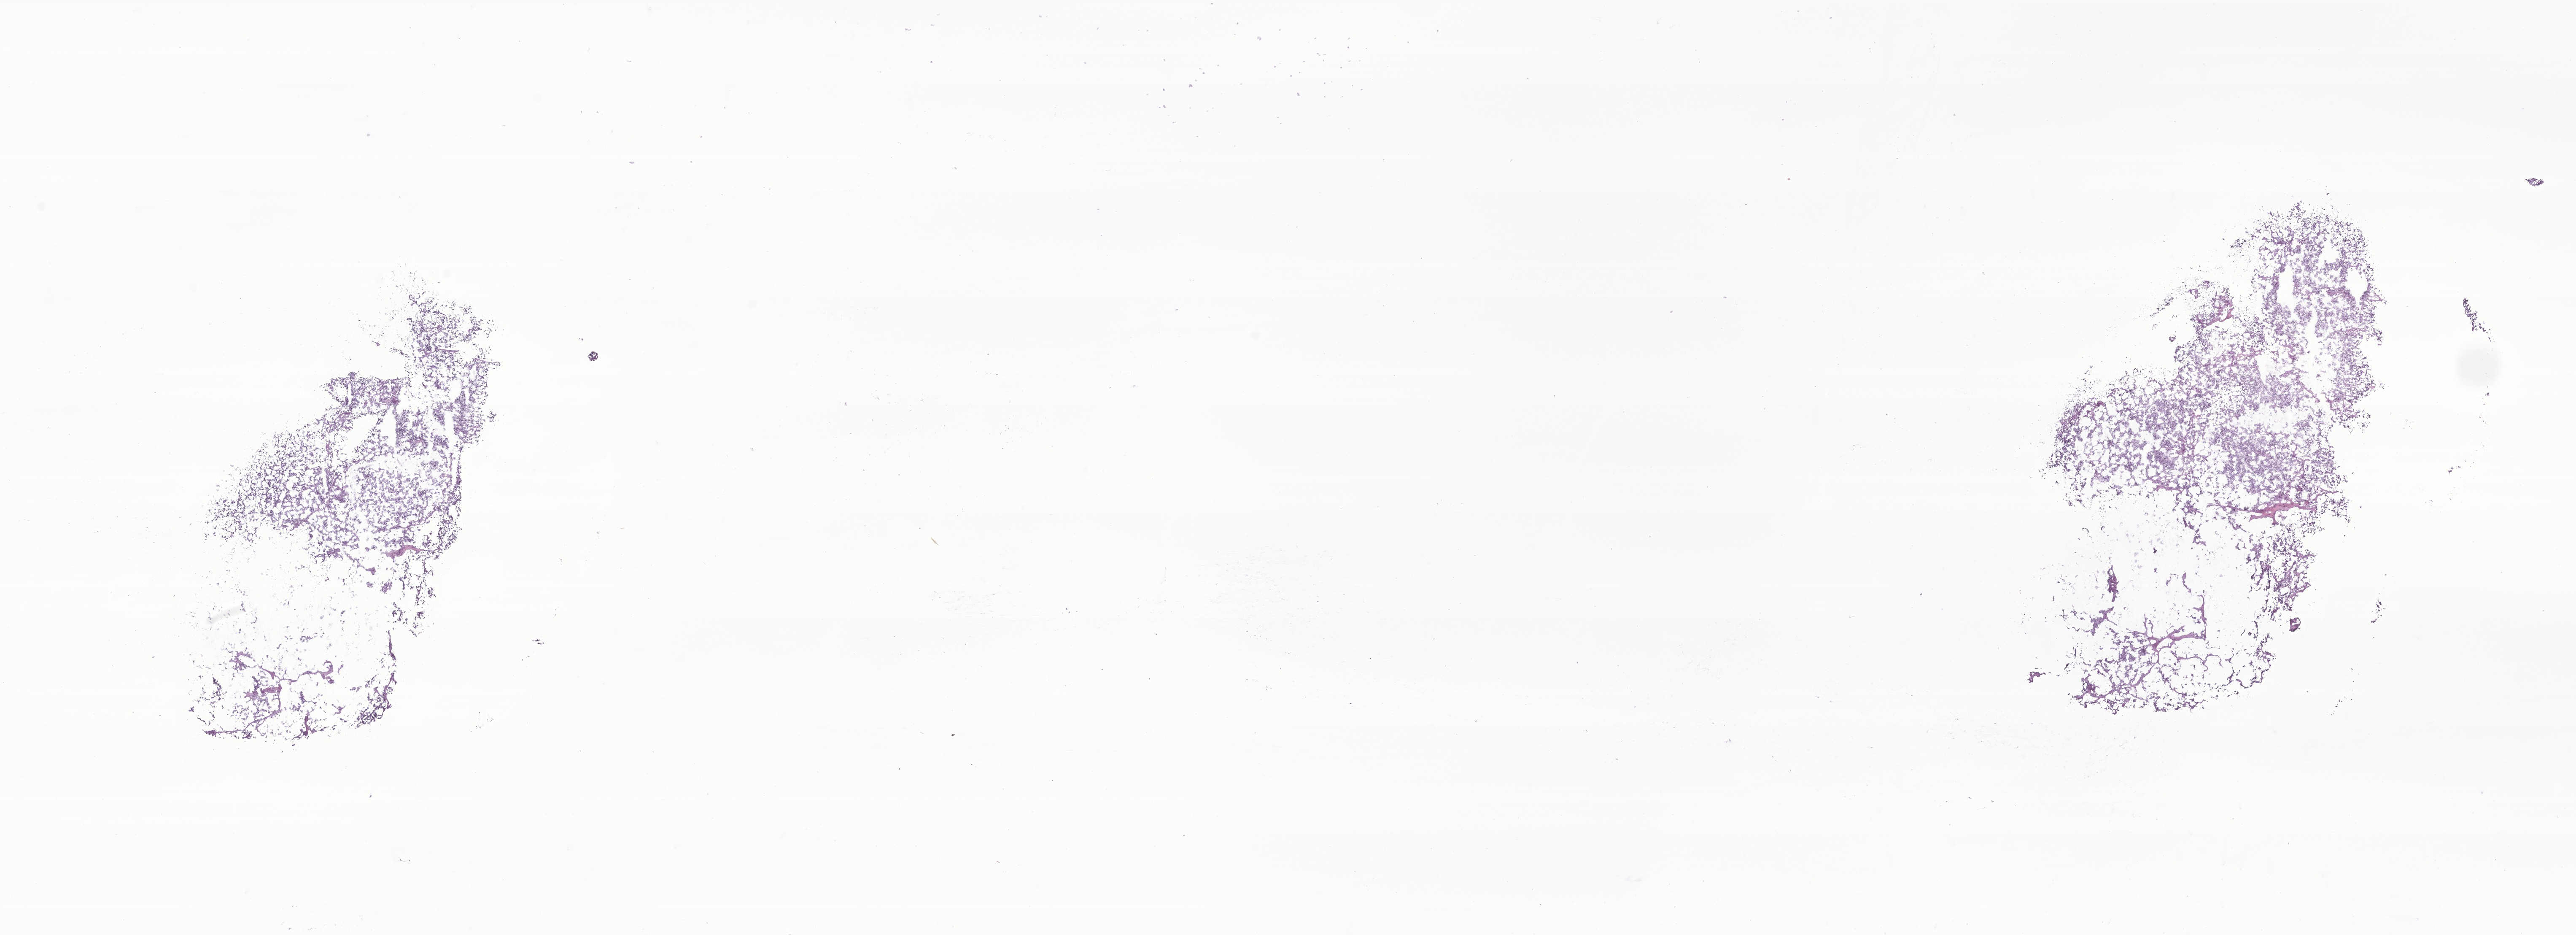
H&E whole-slide image of tumor tissue from the cerebellum — whole scanned area (about 25.8 x 9.3 mm) shown as a low-resolution overview, cryosection (OCT / tissue freezing medium). Patient: male, age 154 months (12 years 10 months).
Recorded diagnosis: Medulloblastoma, NOS.